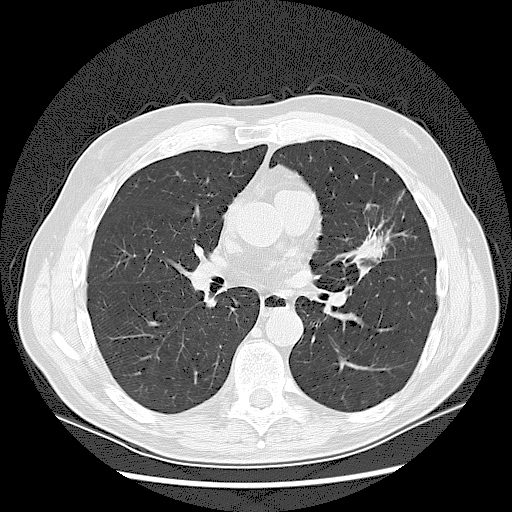
Axial slice from a low-dose chest CT screening exam. Baseline screening round. Lung window (W 1500 / L -600 HU). 2.5 mm slice thickness. Lung (sharp) reconstruction kernel (LUNG). 120 kVp. Slice 64 of 132 in the series. Male participant, aged 65 years at enrolment. Current smoker at enrolment.
- Lesion marked by an expert reader, bounding box (x1, y1, x2, y2) in pixels: (345, 218, 399, 266).
- The exam's reader record, not a measurement of the box and not confirmed to be the same lesion: non-calcified nodule or mass ≥4 mm, left upper lobe, 37 × 27 mm, spiculated (stellate) margins, soft tissue attenuation.
- Participant outcome: lung cancer diagnosed 56 days after this screen — non-small cell carcinoma, poorly differentiated (G3), stage IA (AJCC 6th edition).